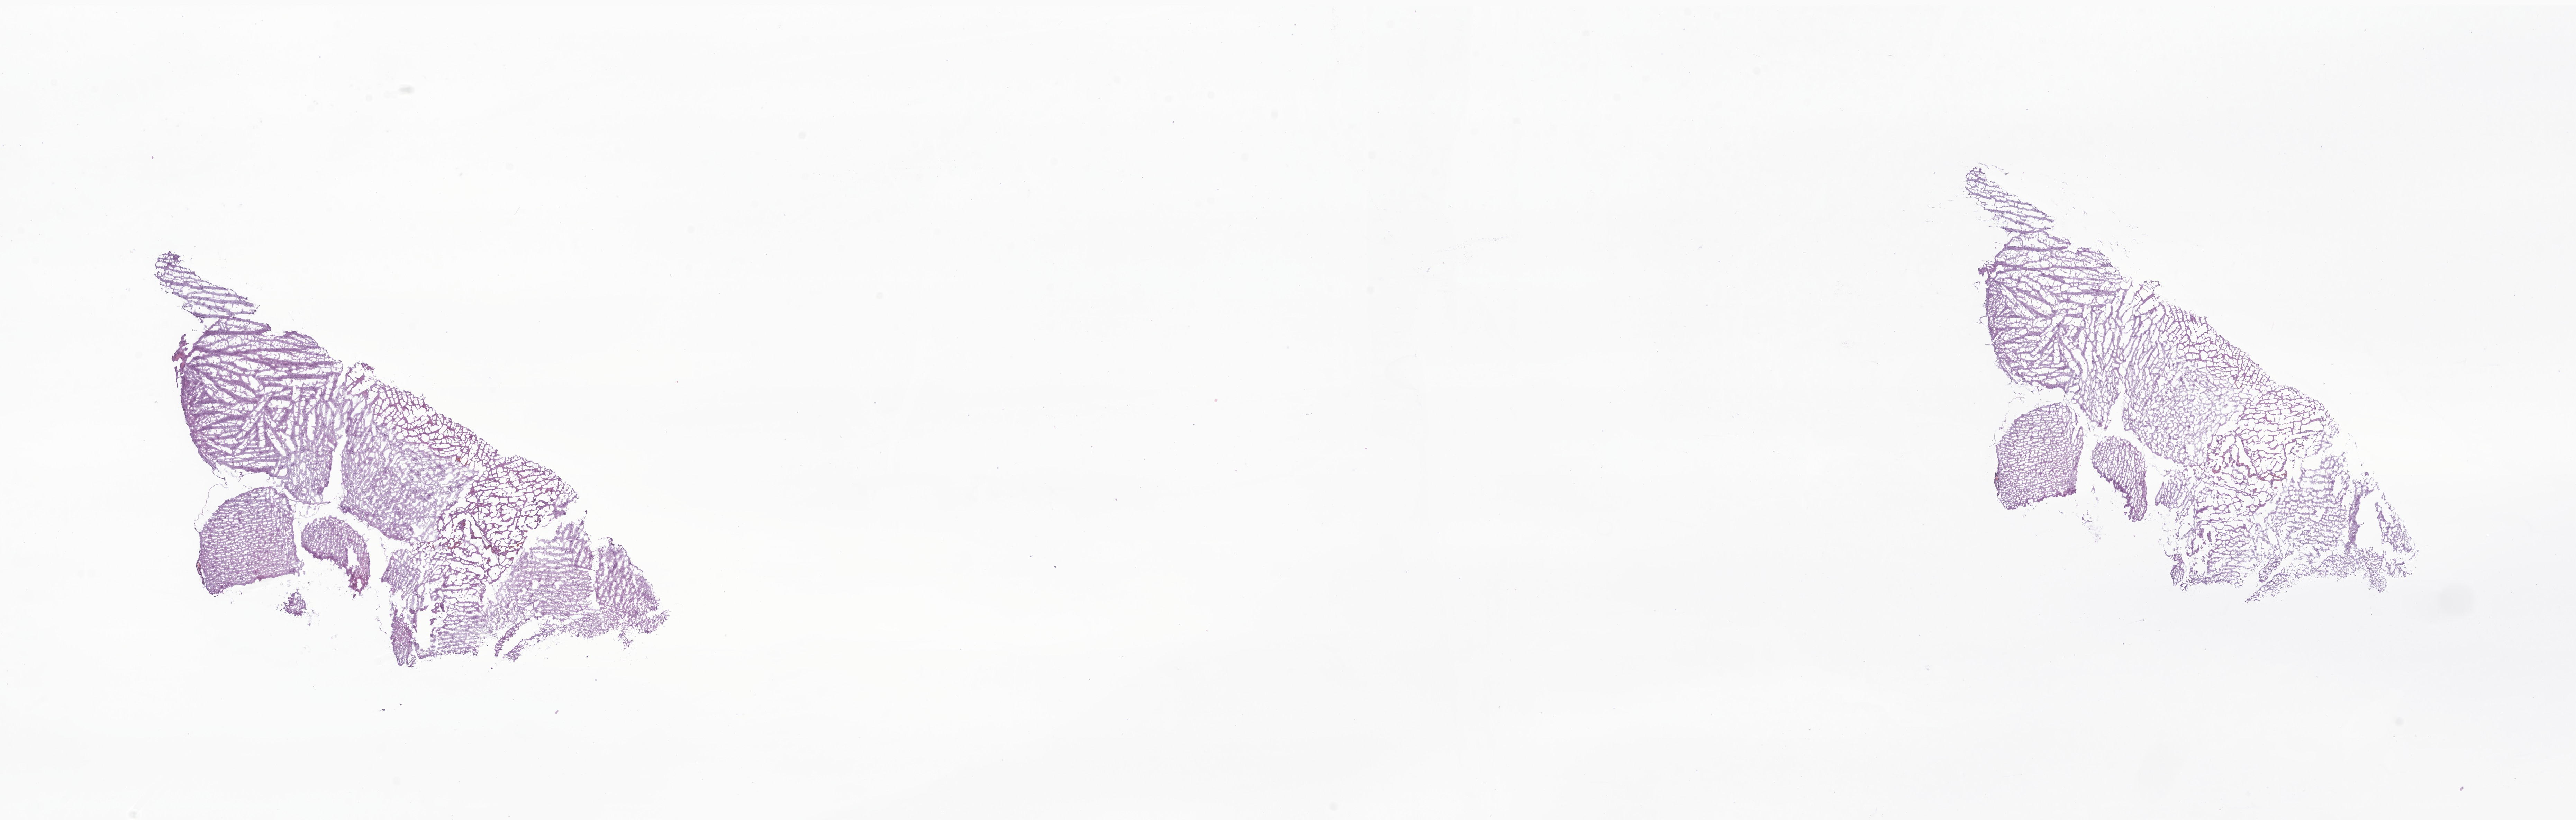
Digitized H&E-stained section of tumor tissue from the brain, a low-resolution overview of the entire scanned area, about 31.4 x 10.0 mm, cryosection (OCT / tissue freezing medium). Female patient, age 187 months.
* diagnosis (ICD-O-3 morphology term): Ganglioglioma, NOS